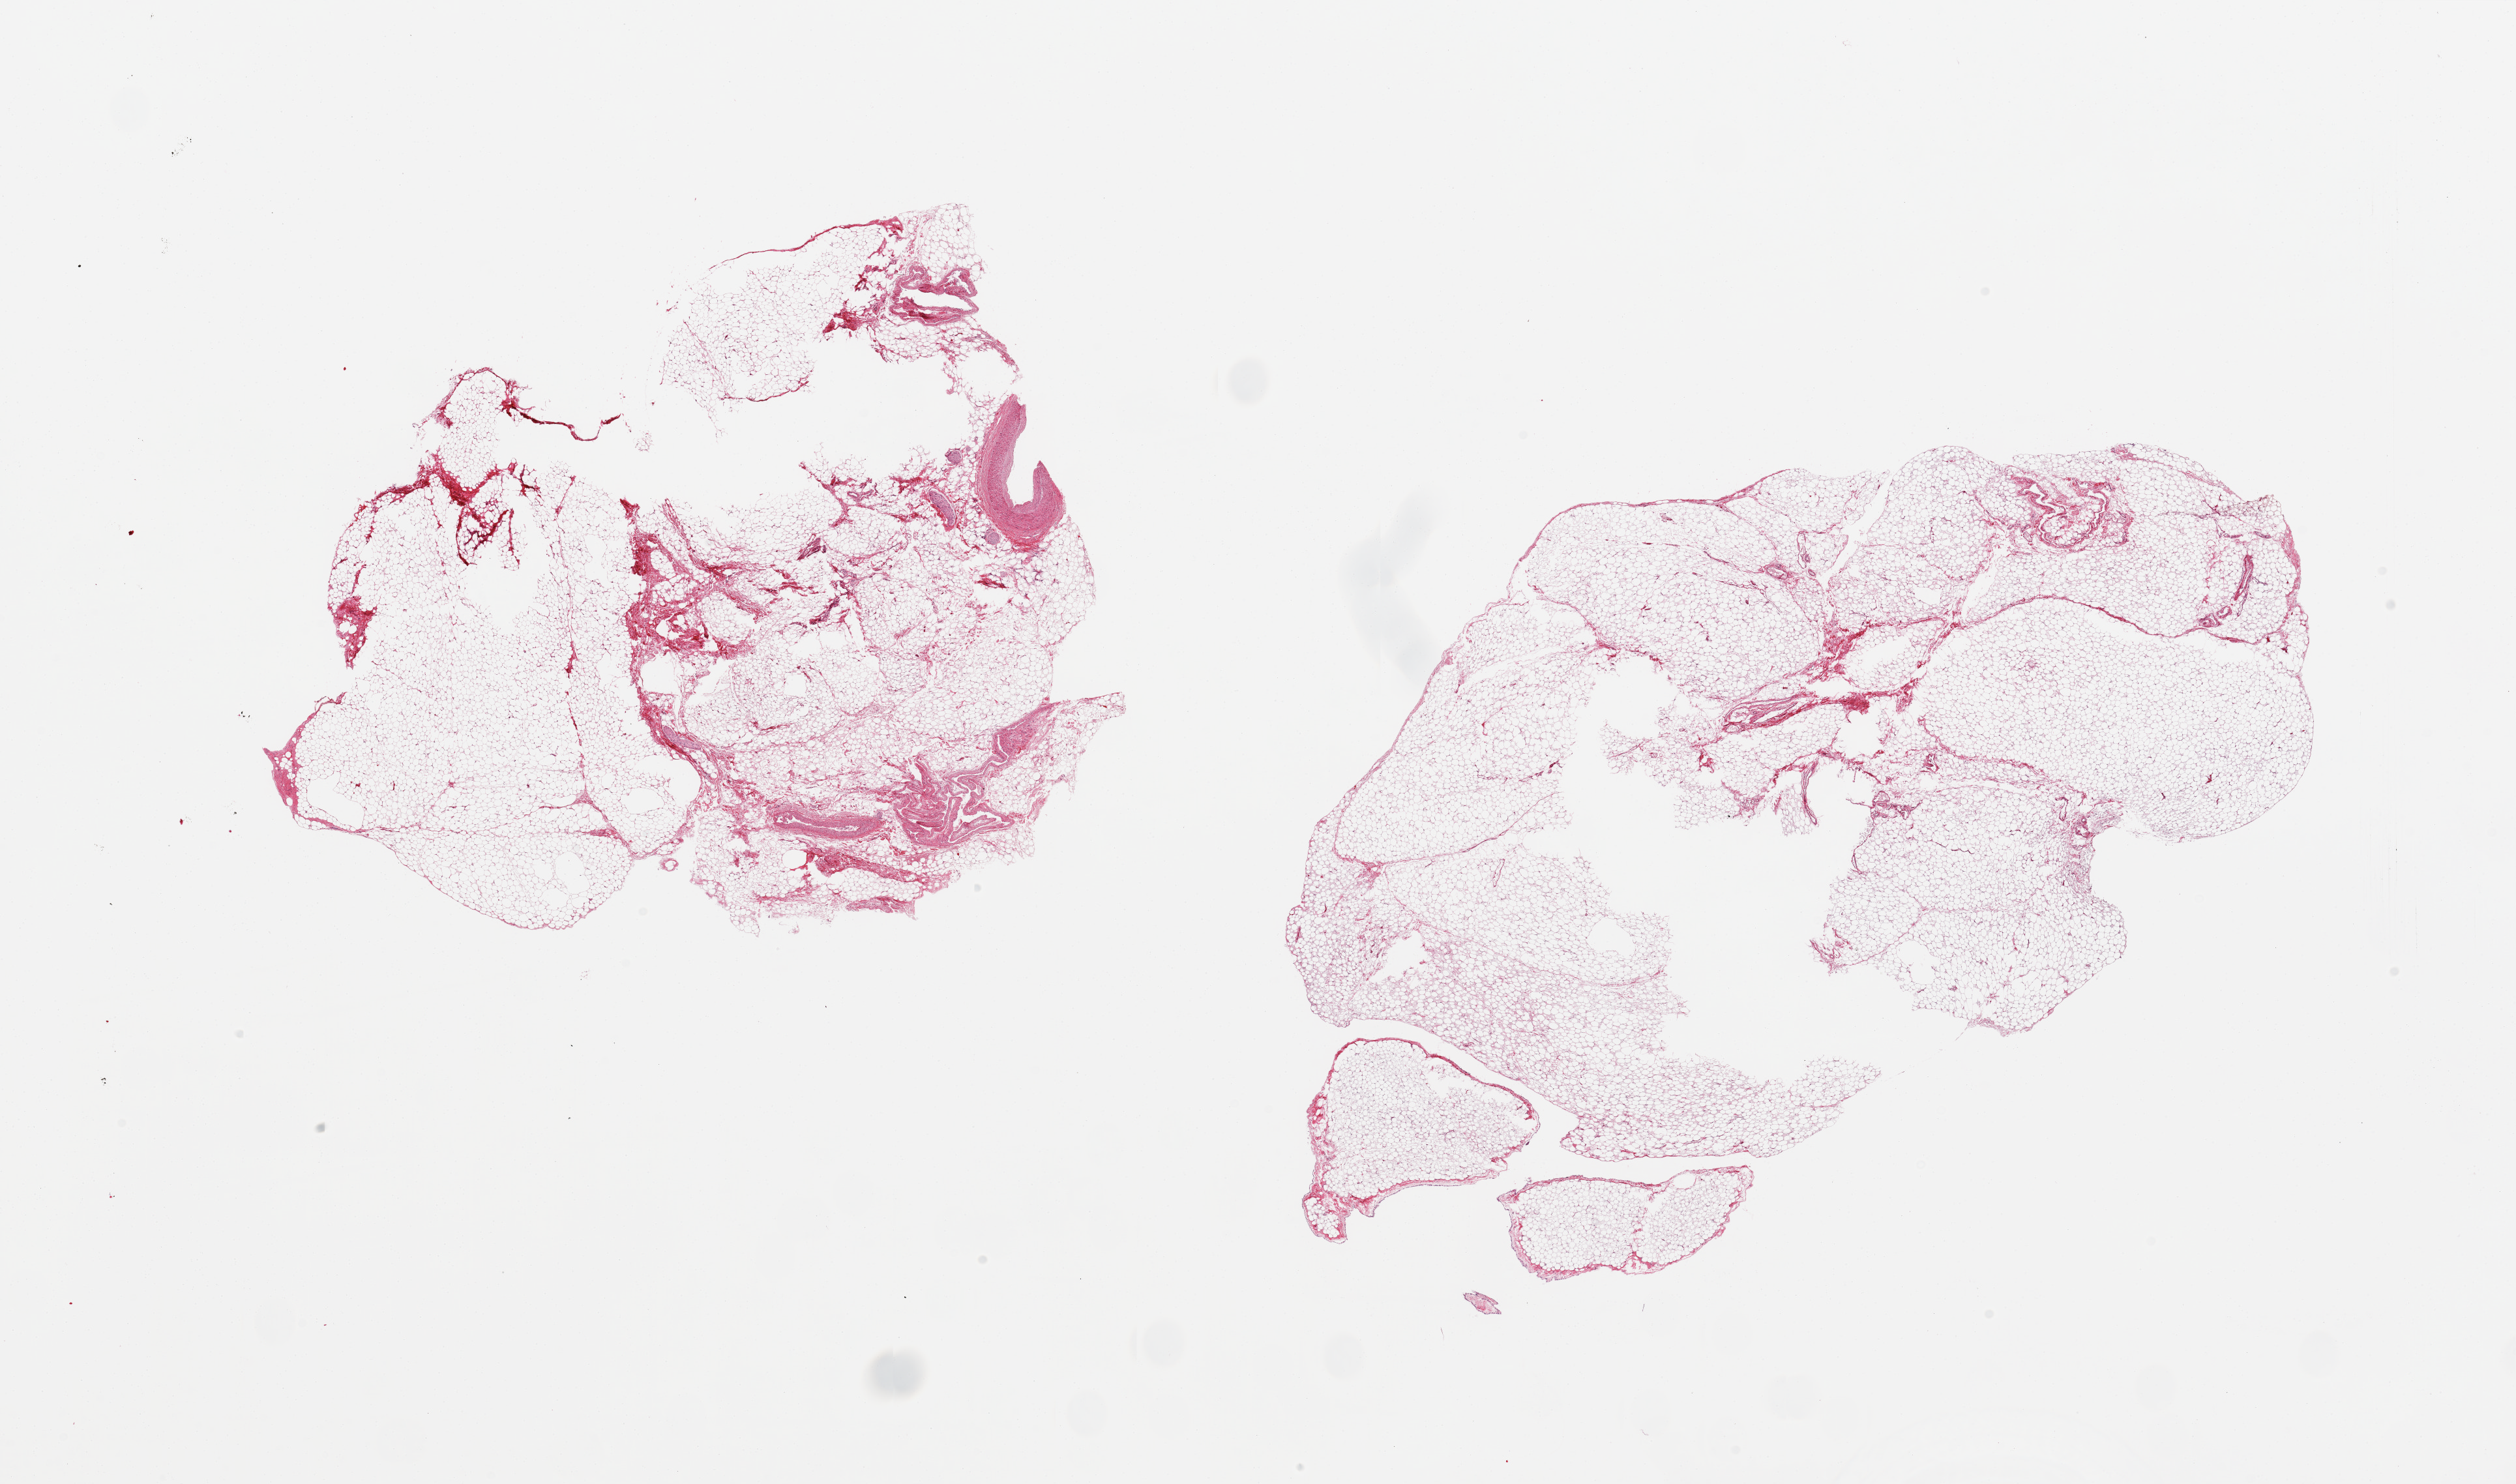
H&E whole-slide image — shown as a low-resolution overview of the whole scanned area (about 30.5 x 18.0 mm); PAXgene-fixed, paraffin-embedded tissue; sampled site (target tissue): omentum; tissue donor sample.
• reviewer comment on this tissue sample: 2 pieces; fat with several large vessels and nerve